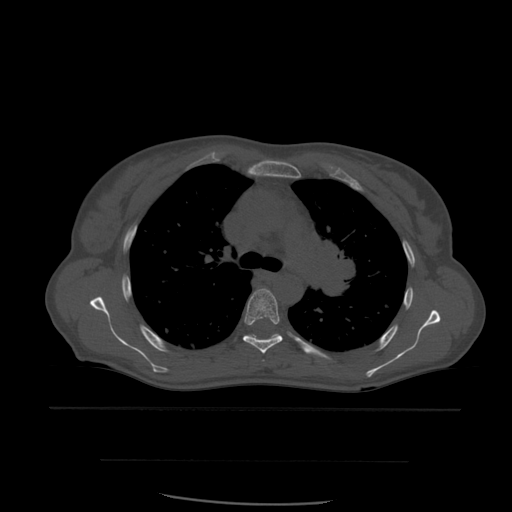
CT including the spine, one axial slice. Slice 409 of 574 in the series (ordered by position). Bone window (W 1800 / L 400 HU). 512 × 512 image matrix. Patient age 48 years. From the clinical record (not read from this slice): primary cancer: lung; vertebrae with lytic lesions (as recorded): T11.
Outlined on this slice (semi-automatically segmented with operator editing):
- T5 vertebra: bounding box [x1, y1, x2, y2] px = [243, 289, 283, 354]
- T6 vertebra: [245, 334, 281, 340]